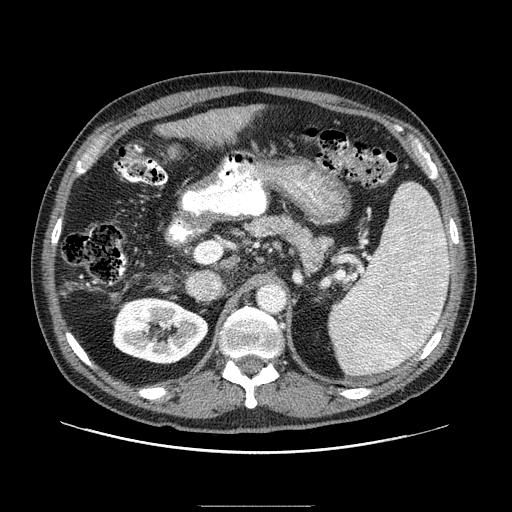
Contrast-enhanced abdominal CT (liver protocol), one axial slice; slice 43 of 99 in the series (ordered by position); reconstruction kernel STANDARD; 100 kVp; one of 2 acquisitions stored at this slice position; soft-tissue window (W 400 / L 40 HU); 512 × 512 image matrix. From the clinical record (not read from this slice): diagnosis: hepatocellular carcinoma (patient treated with transarterial chemoembolisation; whether this scan precedes or follows treatment is not stated here); TNM stage (as recorded): Stage-II; Child-Pugh class: A; tumour nodularity: multinodular.
Annotated regions visible in this slice (semi-automatically segmented with operator editing):
- liver parenchyma outside the tumour (the mass and vessels are separate outlines, so this box may not span the whole liver): bounding box [x1, y1, x2, y2] px = [167, 106, 259, 146]